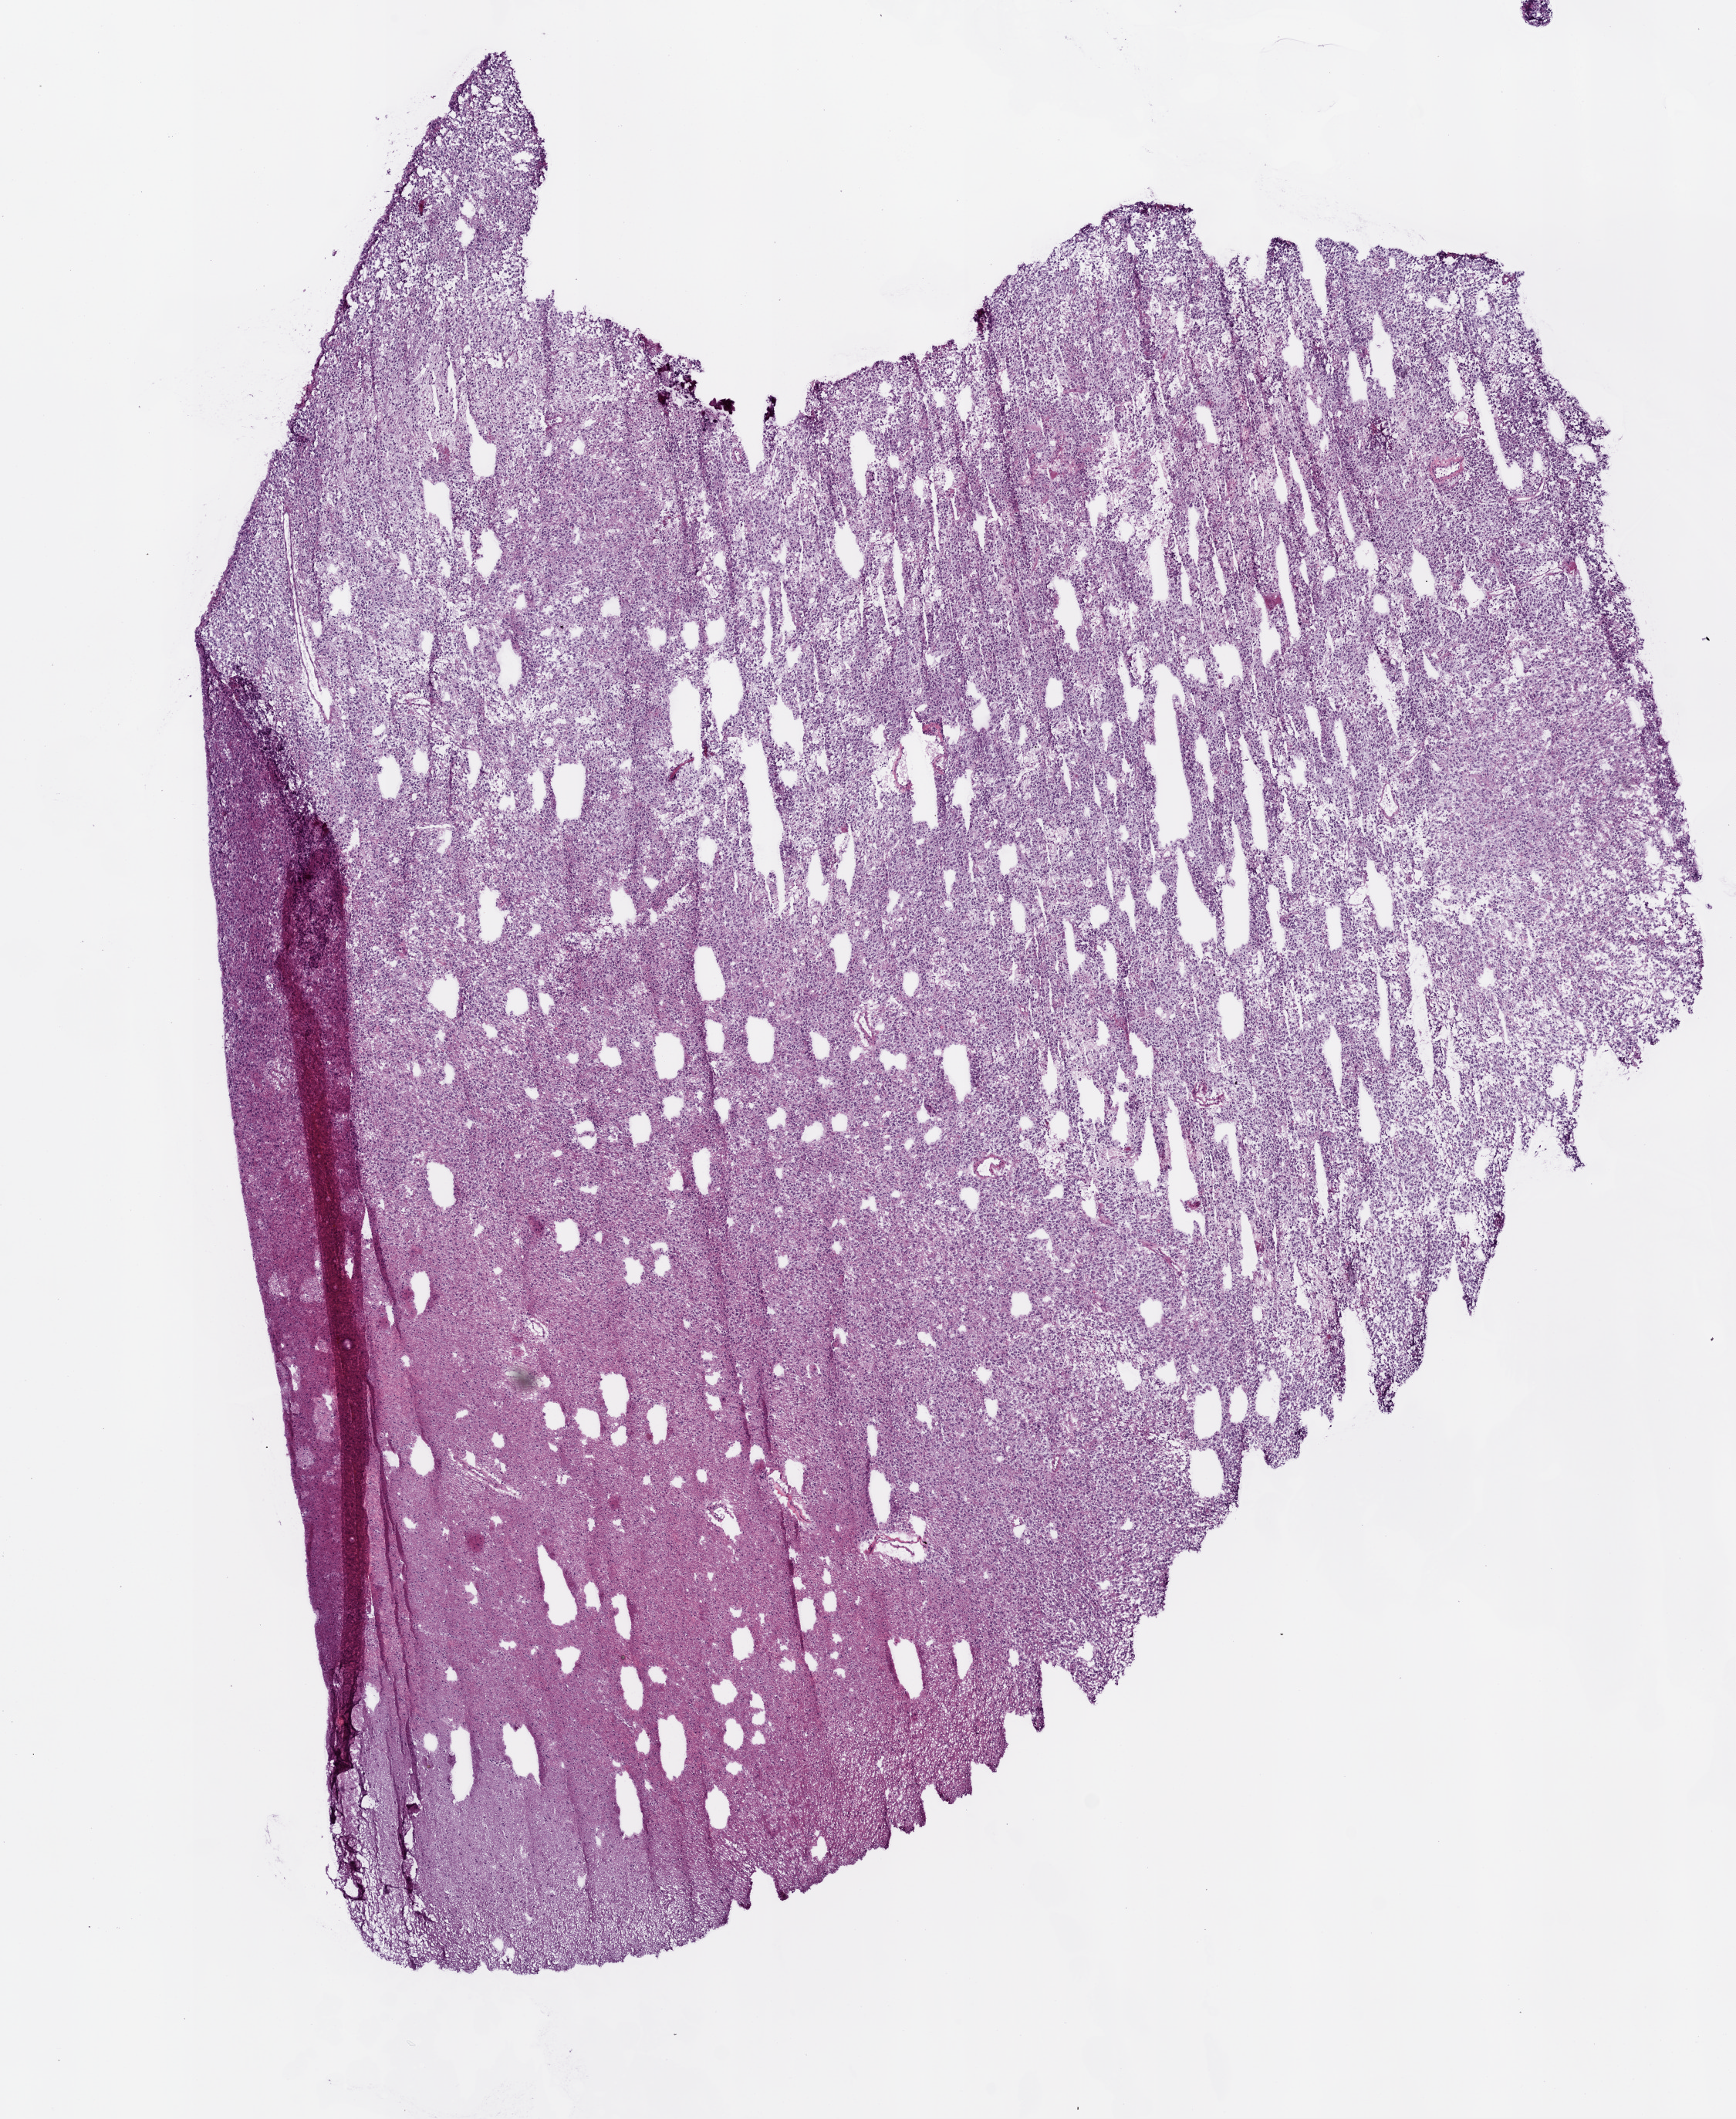
Digitized Hematoxylin and eosin (H&E) stained tissue section (whole slide) — whole scanned area (about 9.0 x 11.0 mm, from a 20x scan) shown as a low-resolution overview, frozen section from the top of the tissue portion, sample: primary tumour, brain. Patient: female, age at initial diagnosis 37 years. Pathologist review of this section (percent, as recorded): tumour cells 100%, tumour nuclei 80%.
Pathologic diagnosis: Mixed glioma.